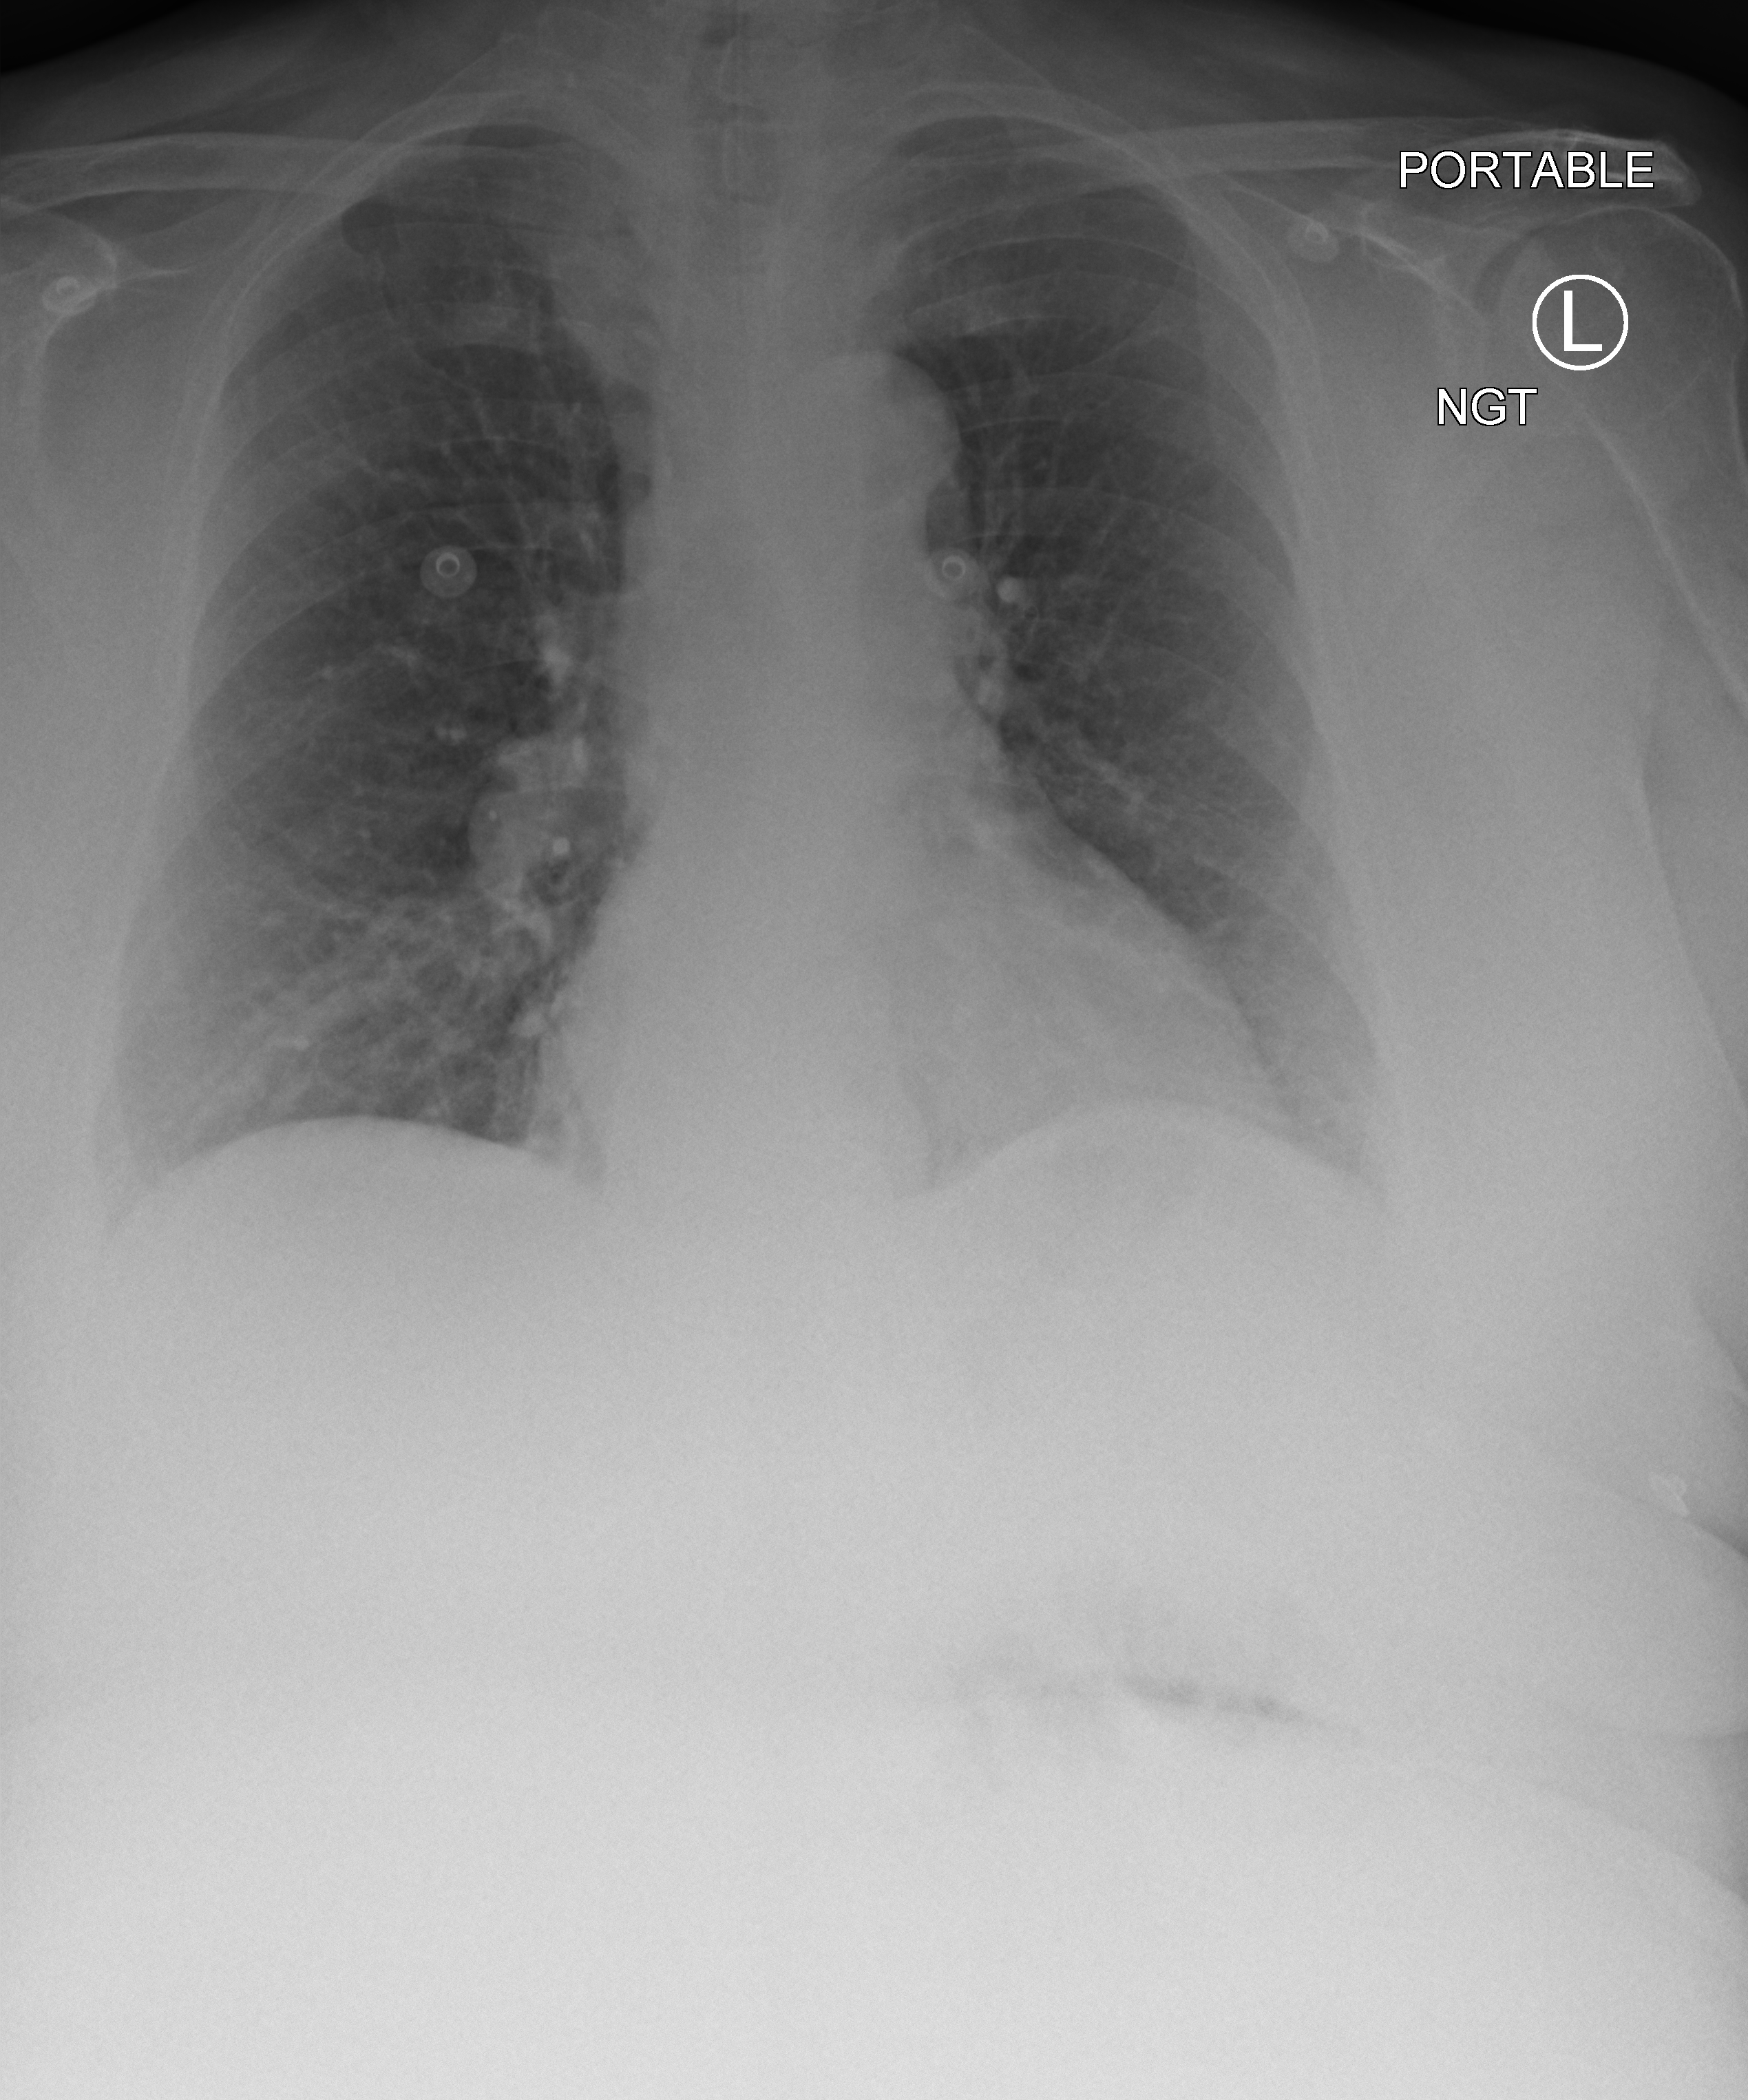
Bedside chest radiograph (computed radiography); anteroposterior (AP) projection. Patient hospitalised with COVID-19; female, aged 60–74 years.
Hospital-stay facts (about this admission, not read from this image; timing relative to this image not recorded): mechanically ventilated during this hospital stay: no.